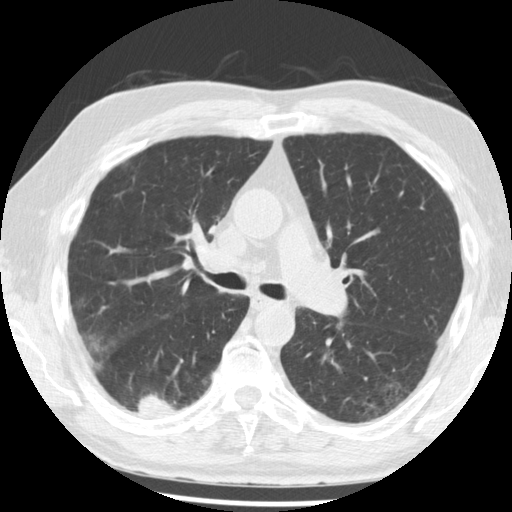
Low-dose screening chest CT, axial slice; third screening round (two years after baseline); lung window (W 1500 / L -600 HU); 2.5 mm slice thickness; standard (soft-tissue) reconstruction kernel (STANDARD); 512 × 512 image matrix. Male, age 68 years at enrolment. Current smoker at enrolment.
Expert reader's lesion annotation, box from (x=120, y=378) to (x=191, y=430) px. The screening reader recorded 3 non-calcified nodules or masses ≥4 mm on this exam (right lower lobe, right lower lobe, right lower lobe); which of them this box marks is not recorded. Lung cancer was diagnosed 48 days after this screen: squamous cell carcinoma, NOS, right lower lobe, moderately differentiated (G2), stage IB (AJCC 6th edition), 20 mm at pathology.